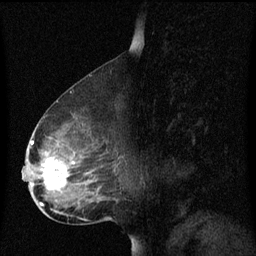
Breast MRI (dynamic contrast-enhanced), one sagittal slice. Slice 38 of 60 in the series (ordered by position). Dynamic contrast-enhanced series, image 2 of 3 at this slice position (ordered by acquisition). 1.5 T. TE 4.2 ms, TR 8.4 ms. 2 mm slice thickness. 256 × 256 image matrix, field of view 200 × 200 mm. Female patient, age 49 years. Case-level facts recorded for this patient, not image findings: setting: breast cancer imaged before/during neoadjuvant chemotherapy; receptor status: HR-positive, HER2-negative.
Outlined on this slice (semi-automatically segmented with operator editing):
- analysis volume of interest (the breast-tissue region the enhancement analysis was run in; not a lesion): box from (x=23, y=126) to (x=116, y=201) px
- tumour enhancement mask (voxels above the 70 % enhancement threshold inside the analysis volume of interest): (x=31, y=140)–(x=75, y=191)